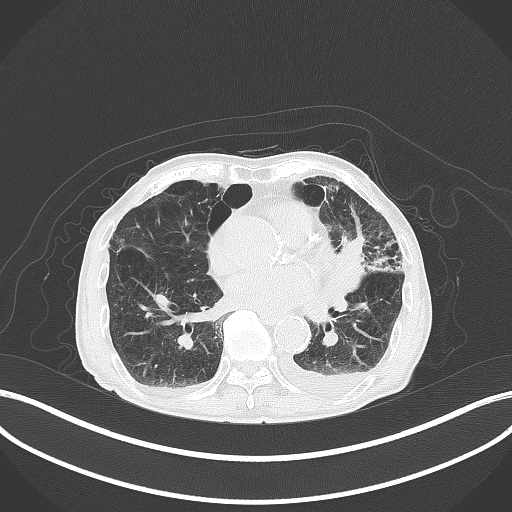
Chest CT, one axial slice; slice 179 of 227 in the series (ordered by position); reconstruction kernel B70f; lung window (W 1500 / L -600 HU); 512 × 512 image matrix, field of view 400 × 400 mm. Male patient, age 90 years or older. Case-level facts recorded for this patient, not image findings: clinical TNM (as recorded): T2b N1 M0.
Structures marked on this image (bounding box drawn by a radiologist):
- lung tumour (recorded histology: squamous cell carcinoma): bounding box [x1, y1, x2, y2] px = [330, 235, 364, 301]